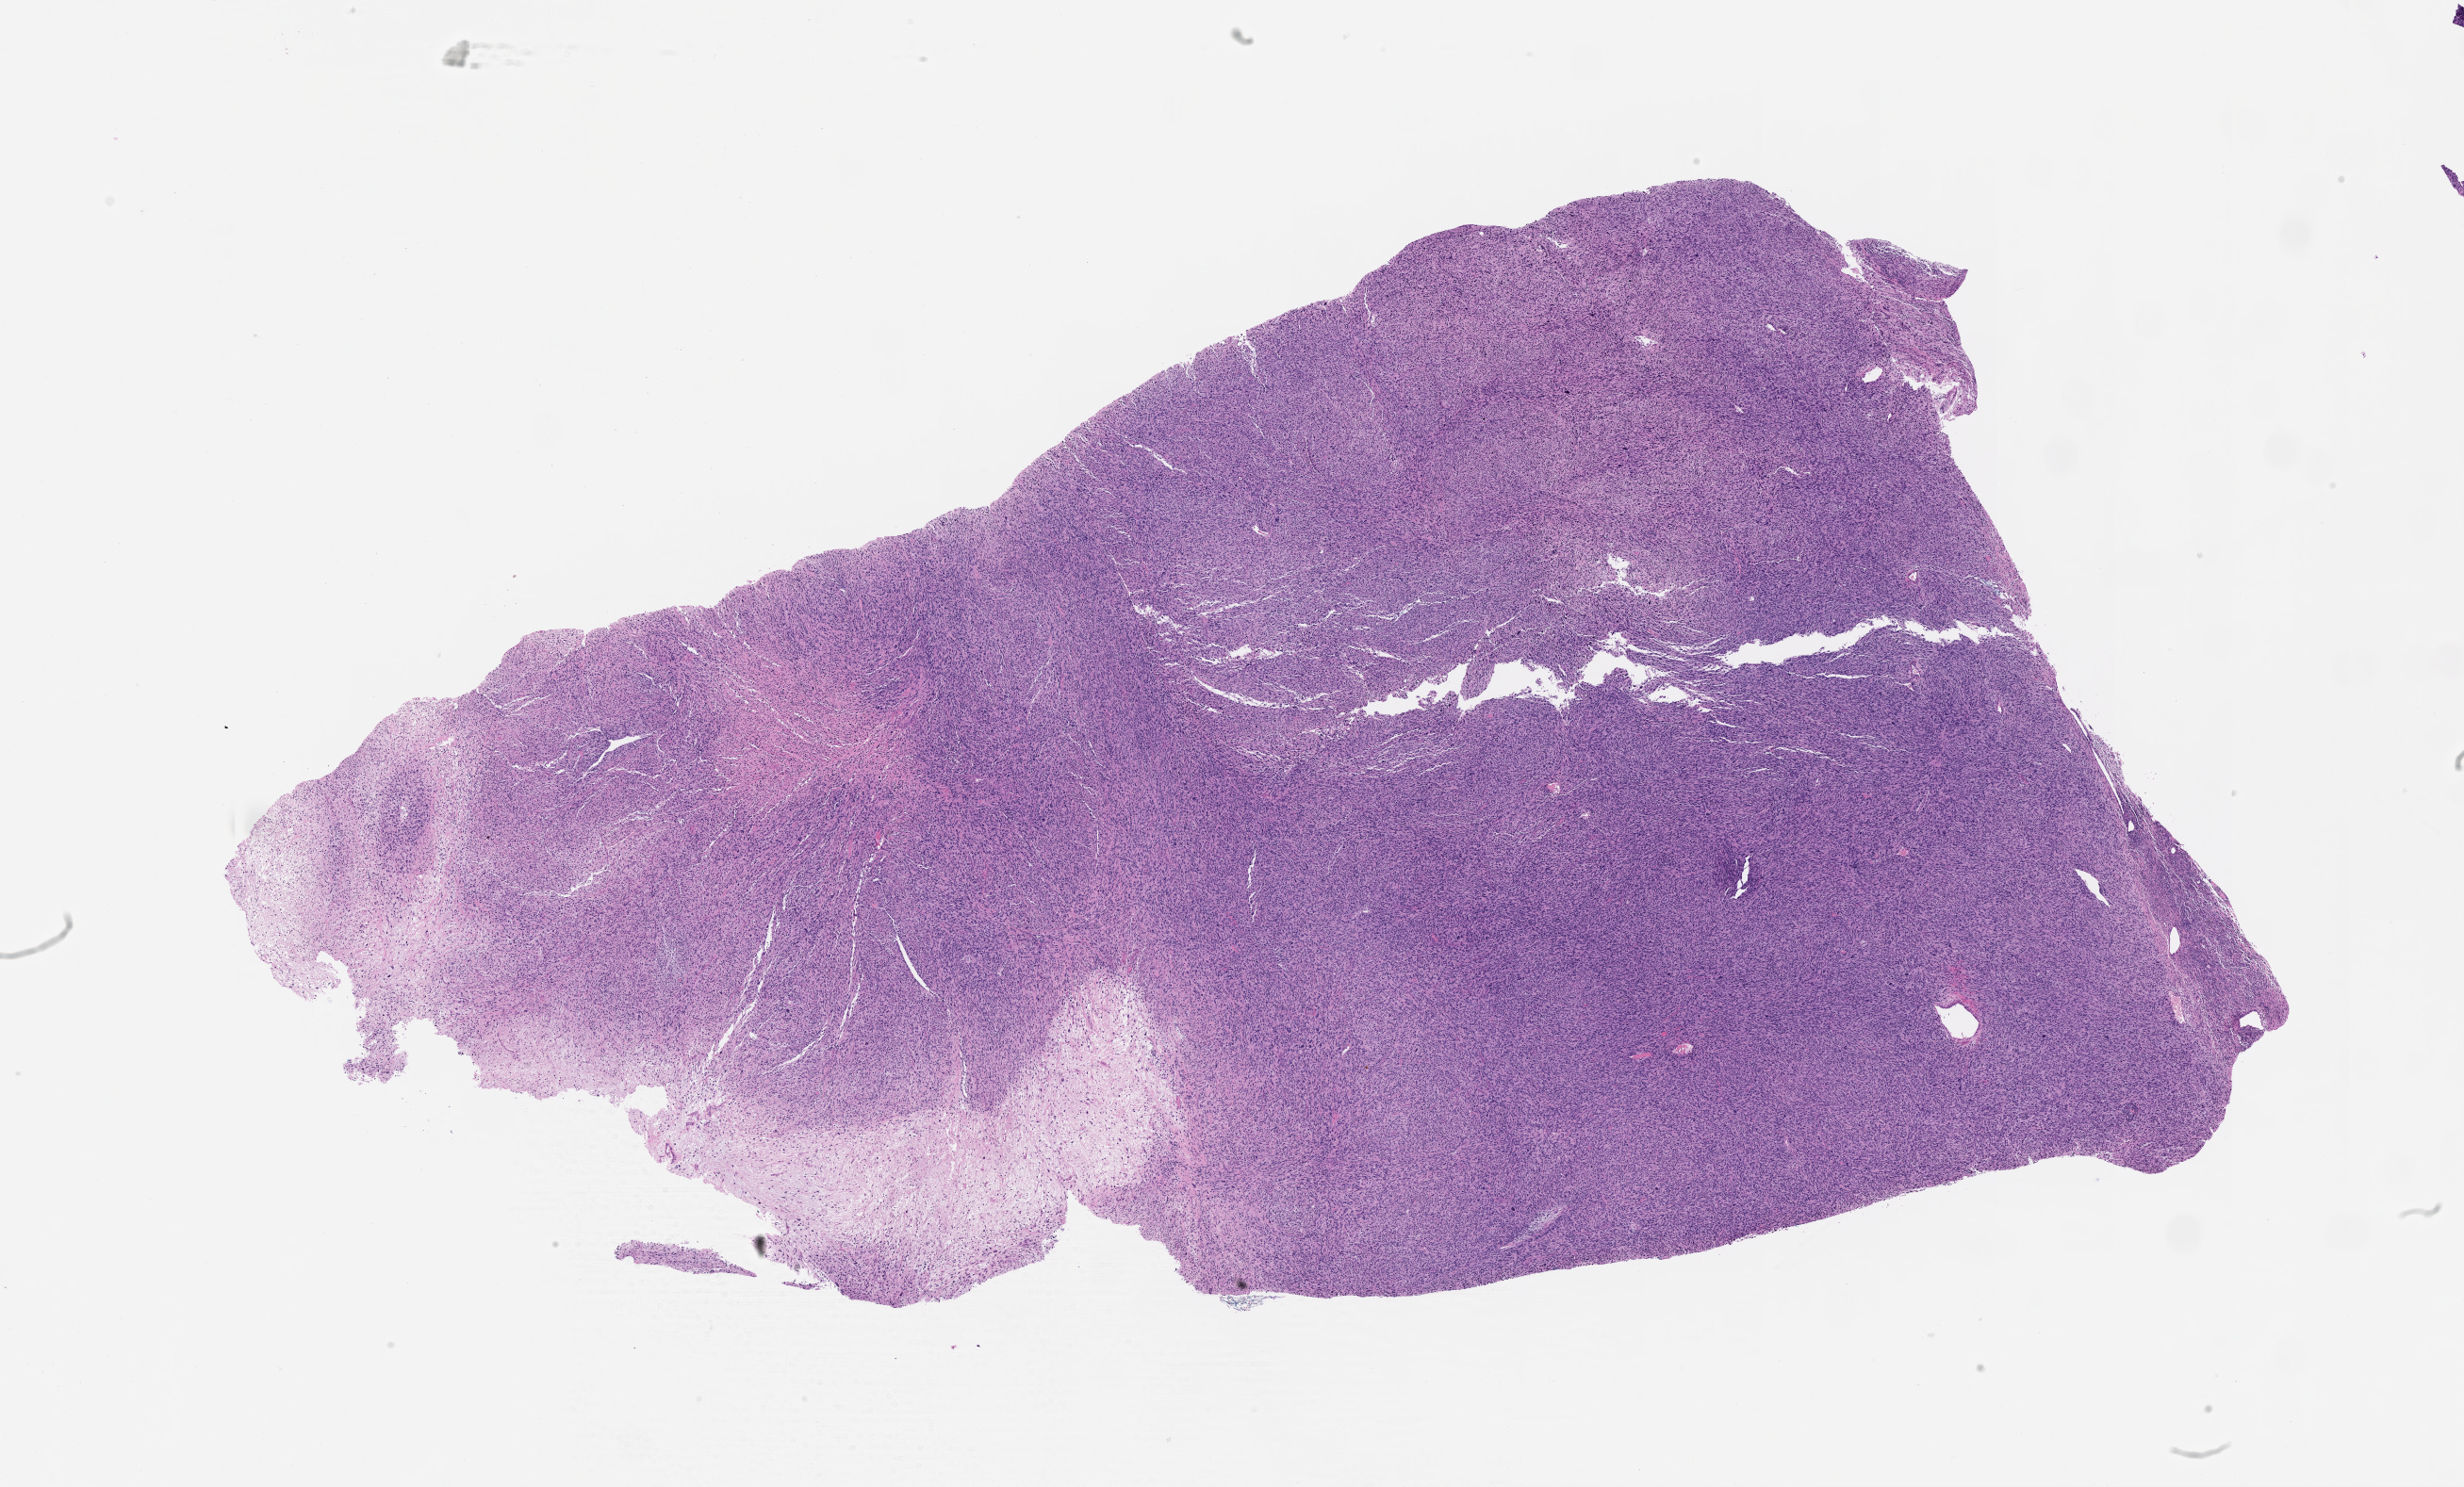
Whole-slide histology image, H&E, a low-resolution overview of the entire scanned area, about 21.0 x 12.7 mm.
Patient diagnosis (cohort enrolment): sarcoma (site not recorded at cohort level).